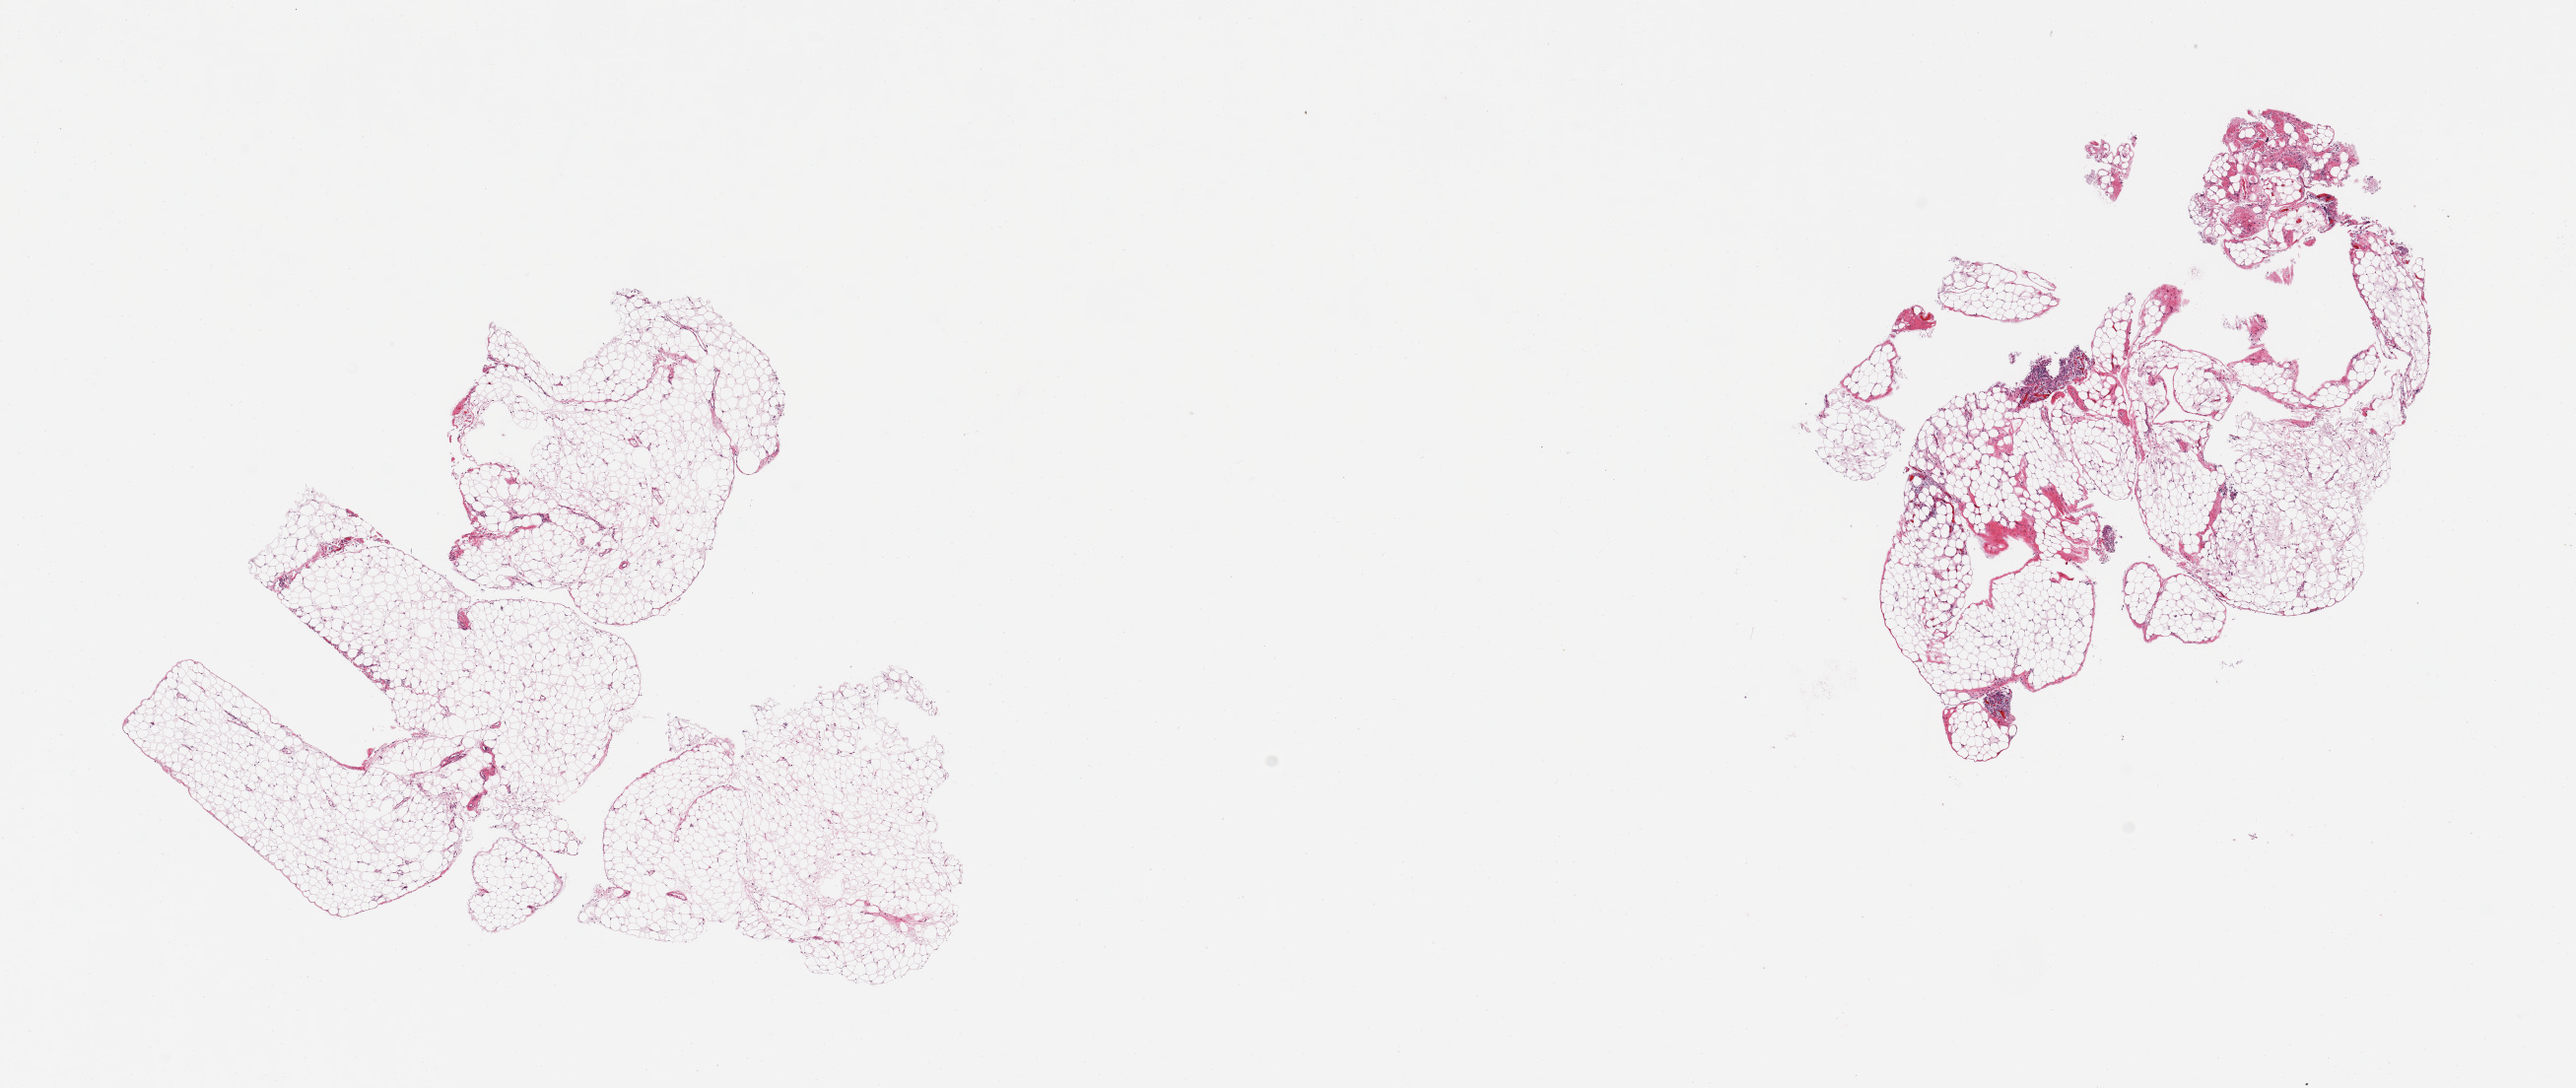
Digitized haematoxylin and eosin-stained section — low-resolution overview of the scanned area, about 20.7 x 8.7 mm (acquisition: 20x scan), PAXgene-fixed paraffin-embedded (PFPE) section, sampled site (target tissue): omentum, tissue donor sample. Male donor.
* reviewer comment on this tissue sample: 2 pieces; lobulated mature adipose tissue